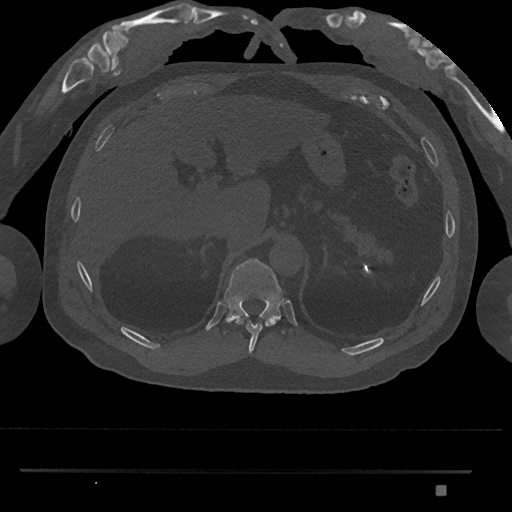
CT including the spine, one axial slice; 120 kVp; bone window (W 1800 / L 400 HU); 0.5 mm slice thickness; 512 × 512 image matrix, field of view 429 × 429 mm. Patient: male, 65 years. Case-level facts recorded for this patient, not image findings: primary cancer: prostate.
Annotated regions visible in this slice (semi-automatic segmentation, software-assisted and operator-edited):
- T10 vertebra: bounding box [x1, y1, x2, y2] px = [236, 319, 275, 355]
- T11 vertebra: [223, 259, 286, 335]